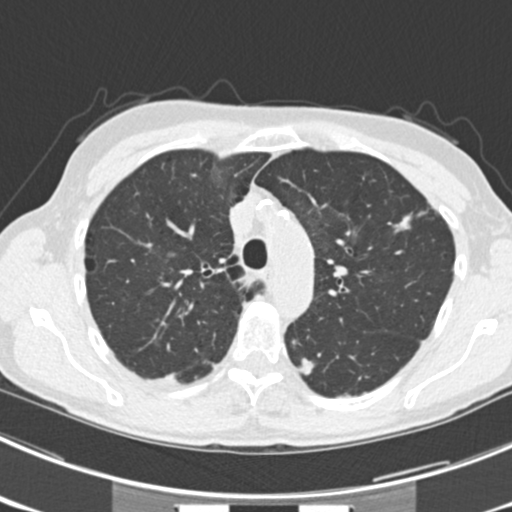
Low-dose screening chest CT, one axial slice. Position 165 of 225 along the scan axis. 120 kVp. Lung window (W 1500 / L -600 HU). 512 × 512 image matrix, field of view 302 × 302 mm.
Annotated regions visible in this slice (outlined manually by an expert reader):
- lesion 2 (tumor, lower lobe of left lung): bounding box [x1, y1, x2, y2] px = [299, 356, 315, 377]